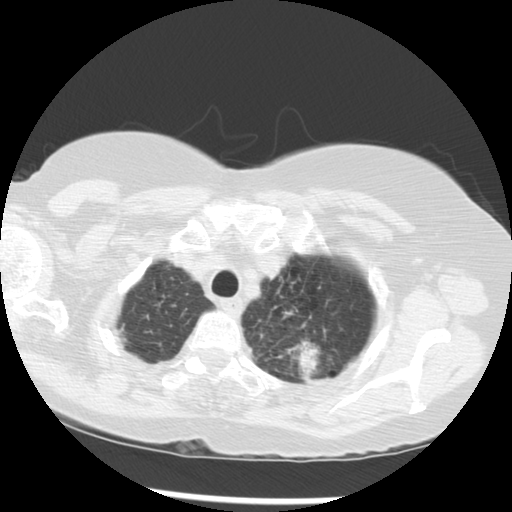
Low-dose screening chest CT, one axial slice. Slice 245 of 283 in the series (ordered by position). Reconstruction kernel STANDARD. 120 kVp. Lung window (W 1500 / L -600 HU). 512 × 512 image matrix, field of view 330 × 330 mm.
Structures marked on this image (manually delineated by an expert):
- lesion 1 (tumor, upper lobe of left lung): bounding box [x1, y1, x2, y2] px = [290, 342, 322, 377]